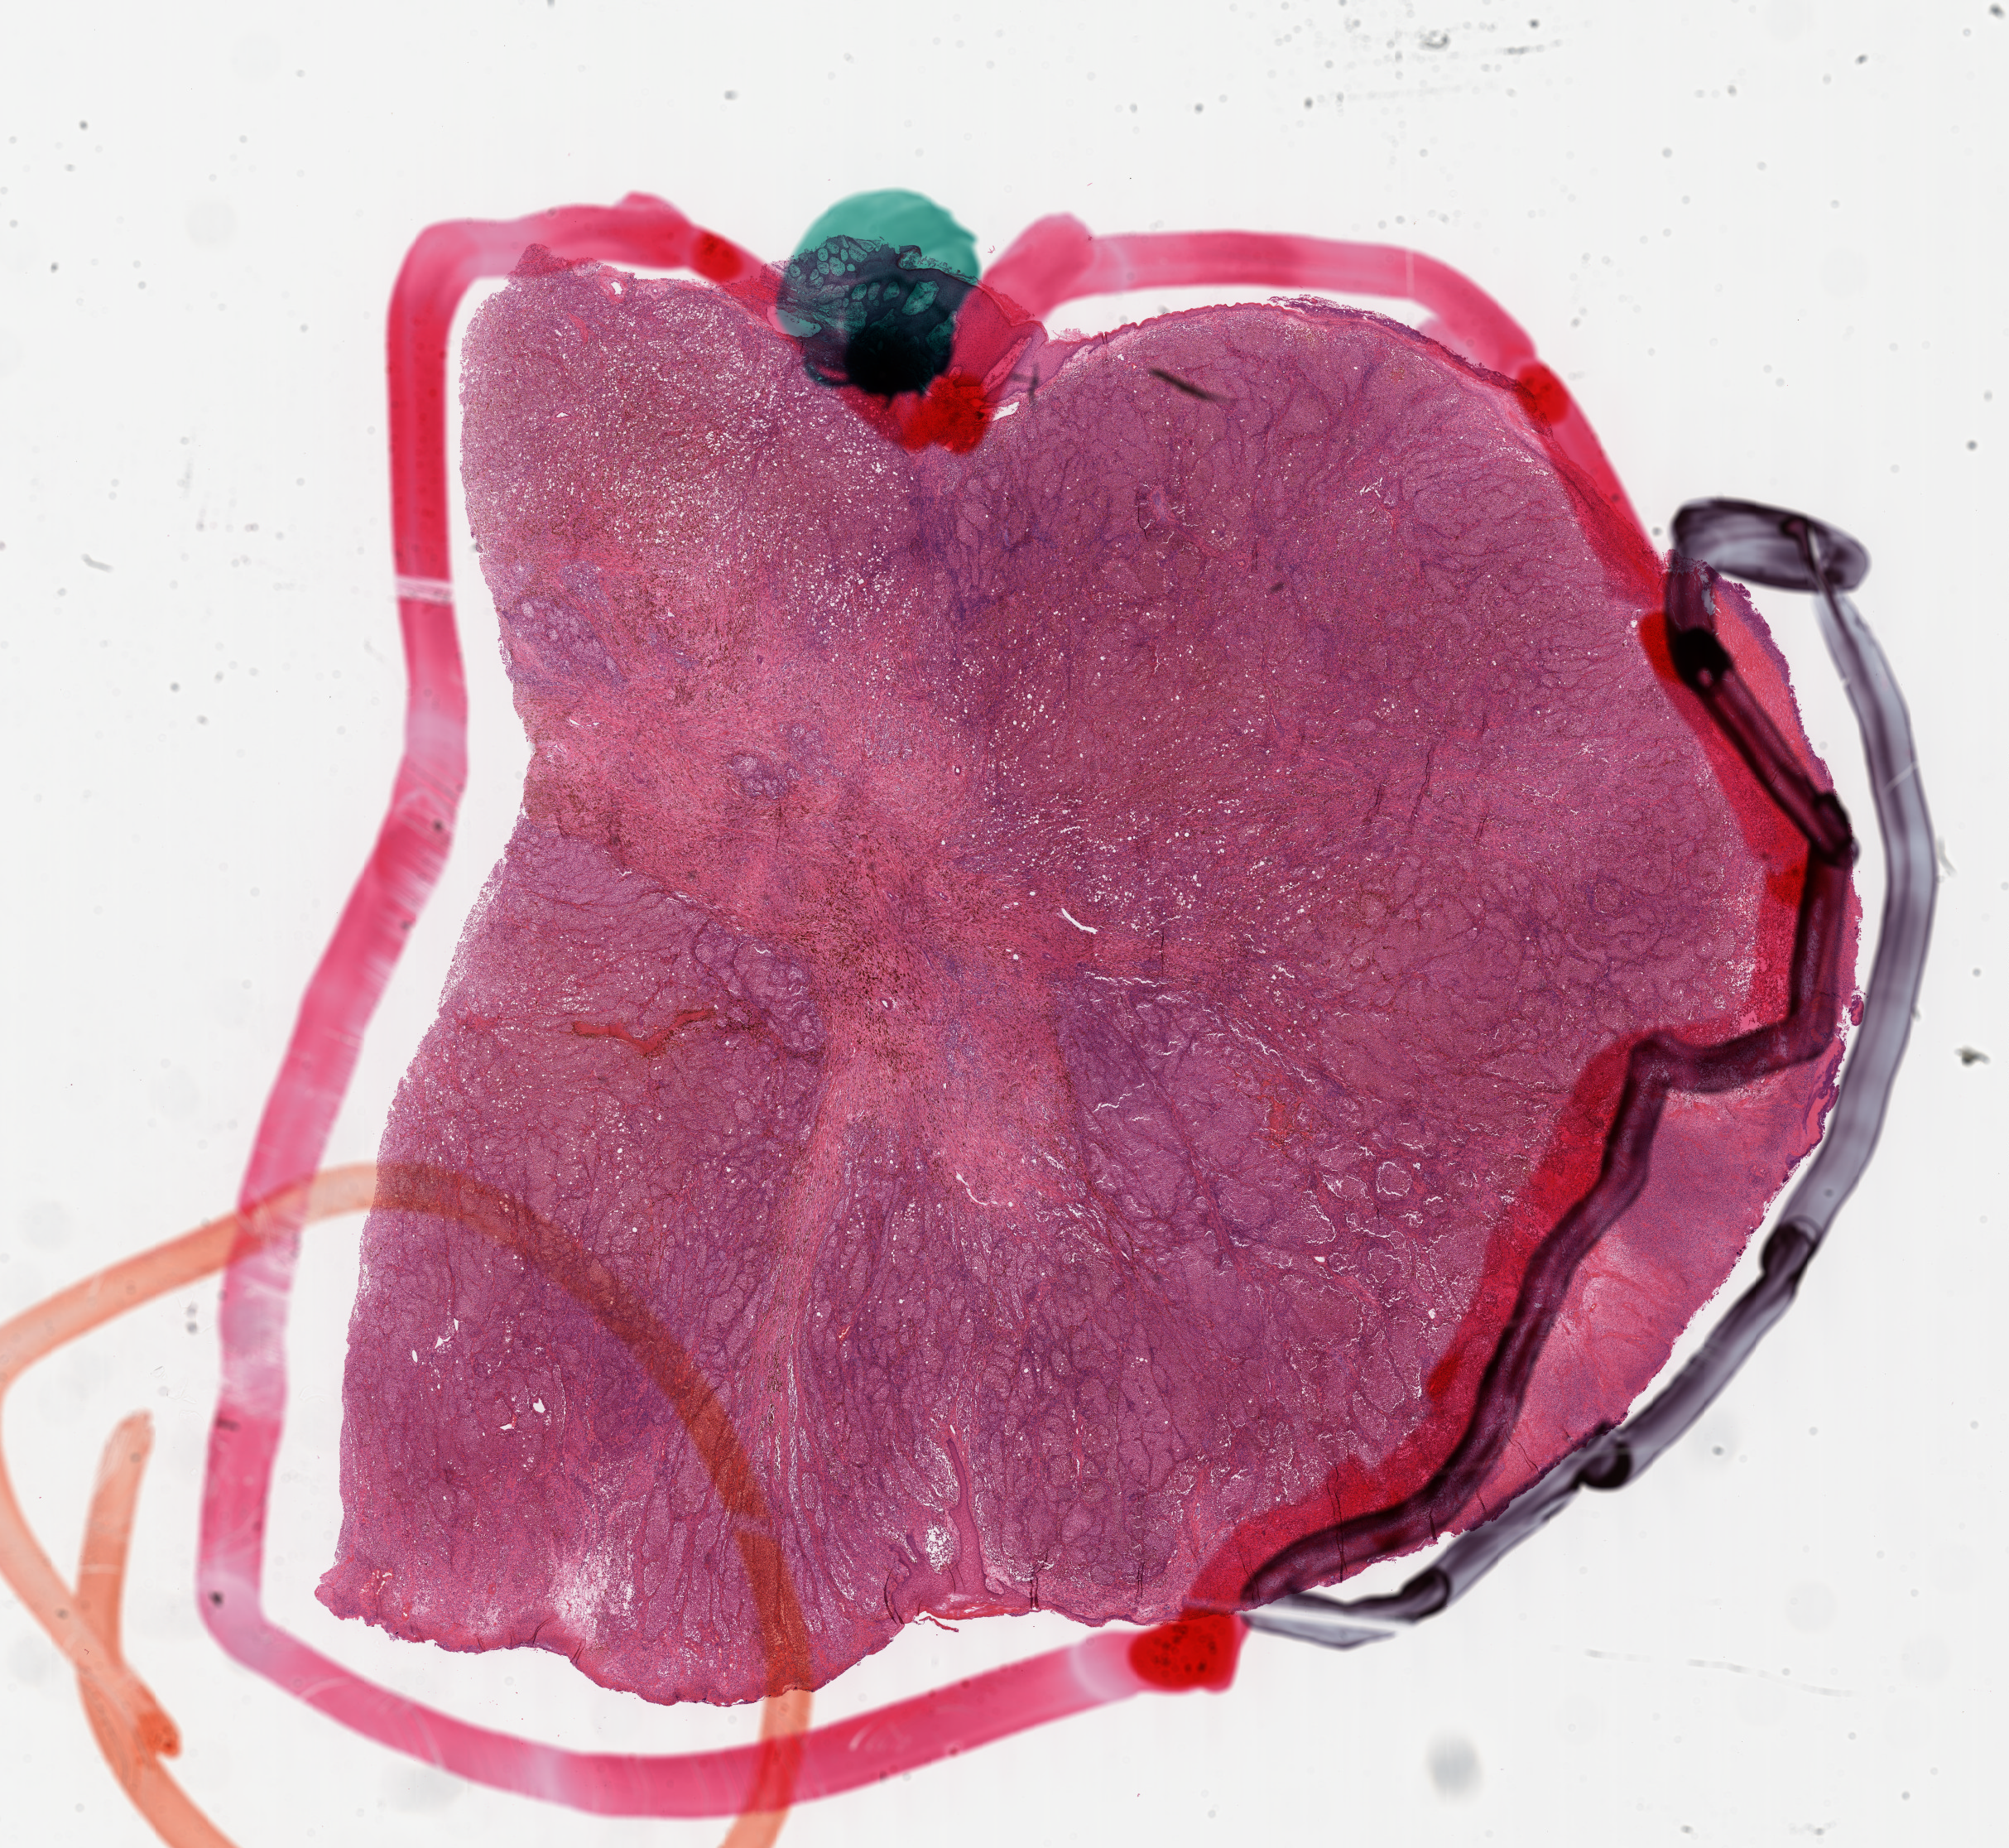
Digitized H&E tissue section (whole slide) — shown as a low-resolution overview of the whole scanned area (about 19.6 x 18.0 mm), FFPE section, skin, primary tumour sample. Patient: male, age at initial diagnosis 66 years.
* AJCC pathologic stage: IIC (7th edition)
* pathologic diagnosis: Malignant melanoma, NOS